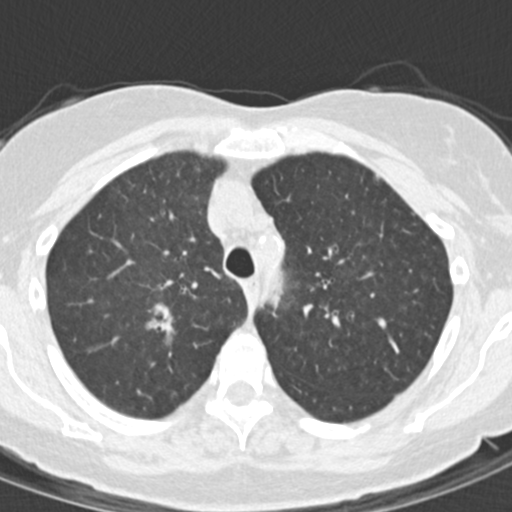
Low-dose screening chest CT, one axial slice. Position 116 of 157 along the scan axis. Reconstruction kernel B30f. 120 kVp. Lung window (W 1500 / L -600 HU). 512 × 512 image matrix.
Outlined on this slice (manually delineated by an expert):
- lesion 1 (tumor, upper lobe of right lung): bounding box <145,302,176,349> (left, top, right, bottom; pixels)